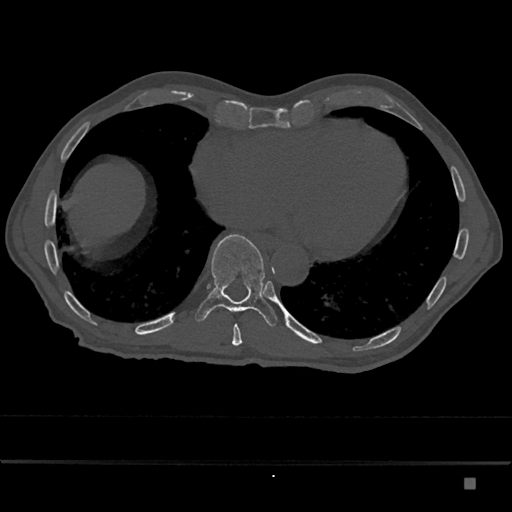
CT including the spine, one axial slice; slice 753 of 797 in the series (ordered by position); reconstruction kernel Br40s/3; bone window (W 1800 / L 400 HU); 512 × 512 image matrix. Patient: male, 72 years. Case-level facts recorded for this patient, not image findings: primary cancer: prostate.
Structures marked on this image (semi-automatically segmented with operator editing):
- T10 vertebra: box from (x=195, y=234) to (x=278, y=327) px
- T9 vertebra: (x=232, y=324)–(x=242, y=346)